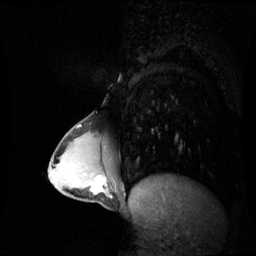
Breast MRI (dynamic contrast-enhanced), one sagittal slice; slice 23 of 60 in the series (ordered by position); dynamic contrast-enhanced series, image 2 of 3 at this slice position (ordered by acquisition); 1.5 T; TE 4.2 ms, TR 8.9 ms; 2.4 mm slice thickness; 256 × 256 image matrix. Patient: female, 34 years. From the clinical record (not read from this slice): setting: breast cancer imaged before/during neoadjuvant chemotherapy; receptor status: triple-negative.
Outlined on this slice (semi-automatically segmented with operator editing):
- analysis volume of interest (the breast-tissue region the enhancement analysis was run in; not a lesion): bounding box <65,168,108,204> (left, top, right, bottom; pixels)
- tumour enhancement mask (voxels above the 70 % enhancement threshold inside the analysis volume of interest): <91,177,105,194>